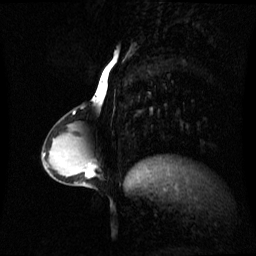
Breast MRI (dynamic contrast-enhanced), one sagittal slice; slice 27 of 60 in the series (ordered by position); dynamic contrast-enhanced series, image 2 of 3 at this slice position (ordered by acquisition); 1.5 T; TE 4.2 ms, TR 8.4 ms; 2.4 mm slice thickness; 256 × 256 image matrix. Patient: female, 34 years. From the clinical record (not read from this slice): setting: breast cancer imaged before/during neoadjuvant chemotherapy; receptor status: triple-negative.
Outlined on this slice (semi-automatically segmented with operator editing):
- analysis volume of interest (the breast-tissue region the enhancement analysis was run in; not a lesion): box from (x=57, y=156) to (x=94, y=187) px
- tumour enhancement mask (voxels above the 70 % enhancement threshold inside the analysis volume of interest): (x=86, y=170)–(x=93, y=177)